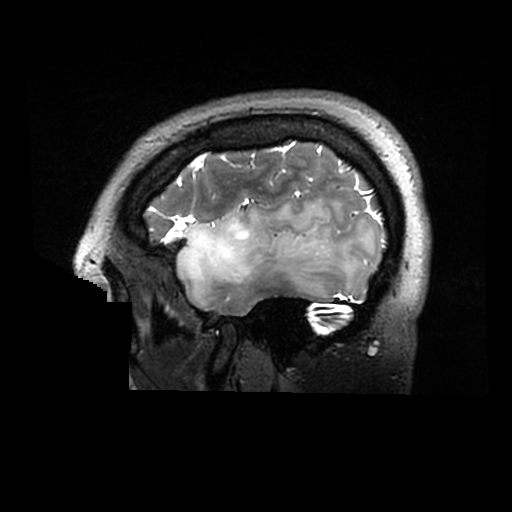
Brain MRI from a brain-tumour surgery series, one sagittal slice. Slice 239 of 320 in the series (ordered by position). 512 × 512 image matrix, field of view 240 × 240 mm. Case-level facts recorded for this patient, not image findings: histopathology: Astrocytoma; WHO grade: 2; IDH mutation: yes.
Structures marked on this image (expert manual segmentation):
- tumour: bounding box <178,200,367,298> (left, top, right, bottom; pixels)